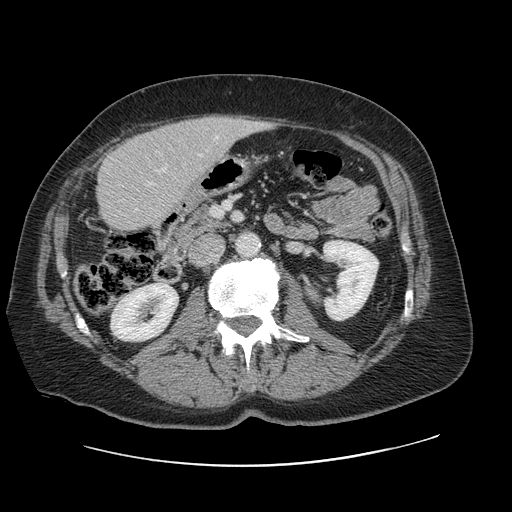
Contrast-enhanced abdominal CT, one axial slice; slice 31 of 138 in the series (ordered by position); intravenous contrast given; soft-tissue window (W 400 / L 40 HU); 512 × 512 image matrix, field of view 402 × 402 mm. Male patient, age 71 years. Case-level facts recorded for this patient, not image findings: diagnosis: colorectal cancer liver metastases, imaged before liver resection; multiple liver metastases: no; largest metastasis: 3.3 cm; chemotherapy before resection: no.
Structures marked on this image (expert manual segmentation):
- hepatic veins: bounding box <200,136,219,156> (left, top, right, bottom; pixels)
- liver: <98,117,263,232>
- planned liver remnant (the part of the liver to remain after resection): <98,133,185,232>
- portal vein (with intrahepatic branches): <158,168,166,172>